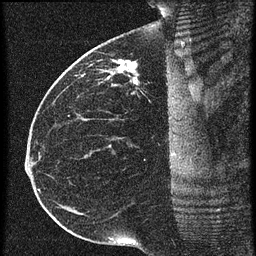
Breast MRI (dynamic contrast-enhanced), one sagittal slice; position 32 of 60 along the scan axis; 3 images stored at this slice position (order not interpretable as contrast timing); 1.5 T; TE 4.2 ms, TR 20.4 ms; 256 × 256 image matrix. Patient: female, 35 years. From the clinical record (not read from this slice): setting: breast cancer imaged before/during neoadjuvant chemotherapy; receptor status: HR-positive, HER2-negative.
Outlined on this slice (semi-automatically segmented with operator editing):
- analysis volume of interest (the breast-tissue region the enhancement analysis was run in; not a lesion): bounding box [x1, y1, x2, y2] px = [84, 50, 179, 97]
- tumour enhancement mask (voxels above the 90 % enhancement threshold inside the analysis volume of interest): [120, 62, 139, 85]